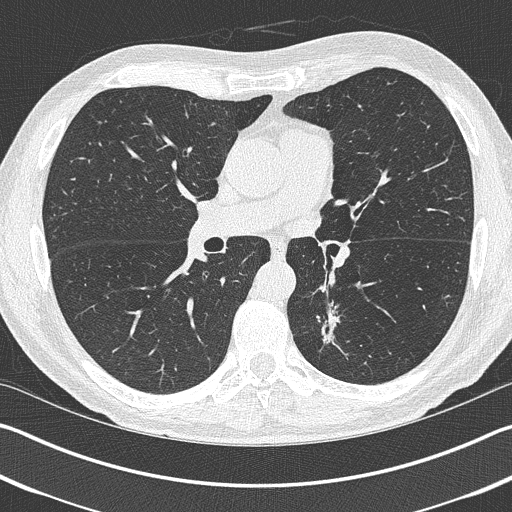
Axial slice from a low-dose chest CT screening exam, baseline annual screen, lung window (W 1500 / L -600 HU), 1 mm slice thickness, slice 175 of 402 in the series, 512 × 512 image matrix. Male participant, aged 69 years at enrolment. Current smoker at enrolment.
Expert-annotated lung lesion, box from (x=294, y=305) to (x=351, y=363) px. The exam's reader record, not a measurement of the box and not confirmed to be the same lesion: non-calcified nodule or mass ≥4 mm, left upper lobe, 19 × 19 mm, spiculated (stellate) margins, pre-existing on the prior screen: yes. Lung cancer was diagnosed 202 days after this screen: non-small cell carcinoma, left lower lobe, stage IIIA (AJCC 6th edition), 20 mm at pathology.